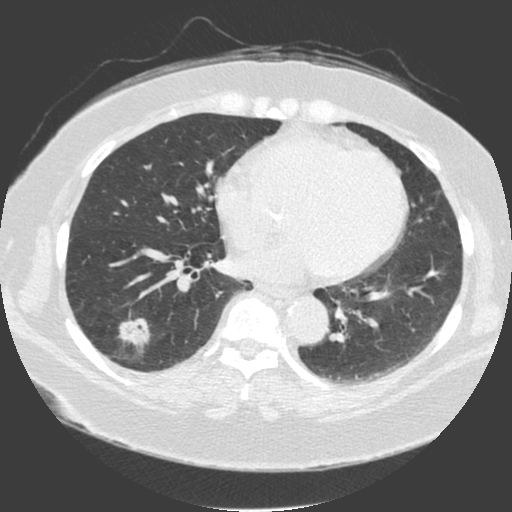
Low-dose screening chest CT, one axial slice; position 78 of 175 along the scan axis; lung window (W 1500 / L -600 HU); 512 × 512 image matrix, field of view 370 × 370 mm.
Structures marked on this image (manually delineated by an expert):
- lesion 1 (tumor, lower lobe of right lung): bounding box <119,319,149,346> (left, top, right, bottom; pixels)